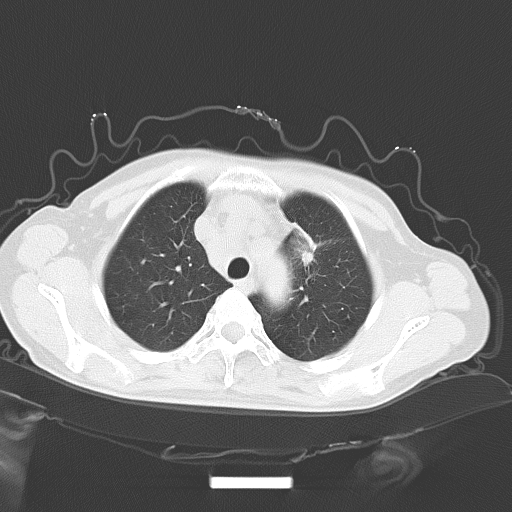
Chest CT, one axial slice; position 43 of 54 along the scan axis; reconstruction kernel B70f; 120 kVp; lung window (W 1500 / L -600 HU); 512 × 512 image matrix. Patient: female, 50 years. Case-level facts recorded for this patient, not image findings: clinical TNM (as recorded): T2a N1 M1c.
Annotated regions visible in this slice (rectangle marked by the reading radiologist):
- lung tumour (recorded histology: adenocarcinoma): bounding box [x1, y1, x2, y2] px = [288, 218, 321, 271]